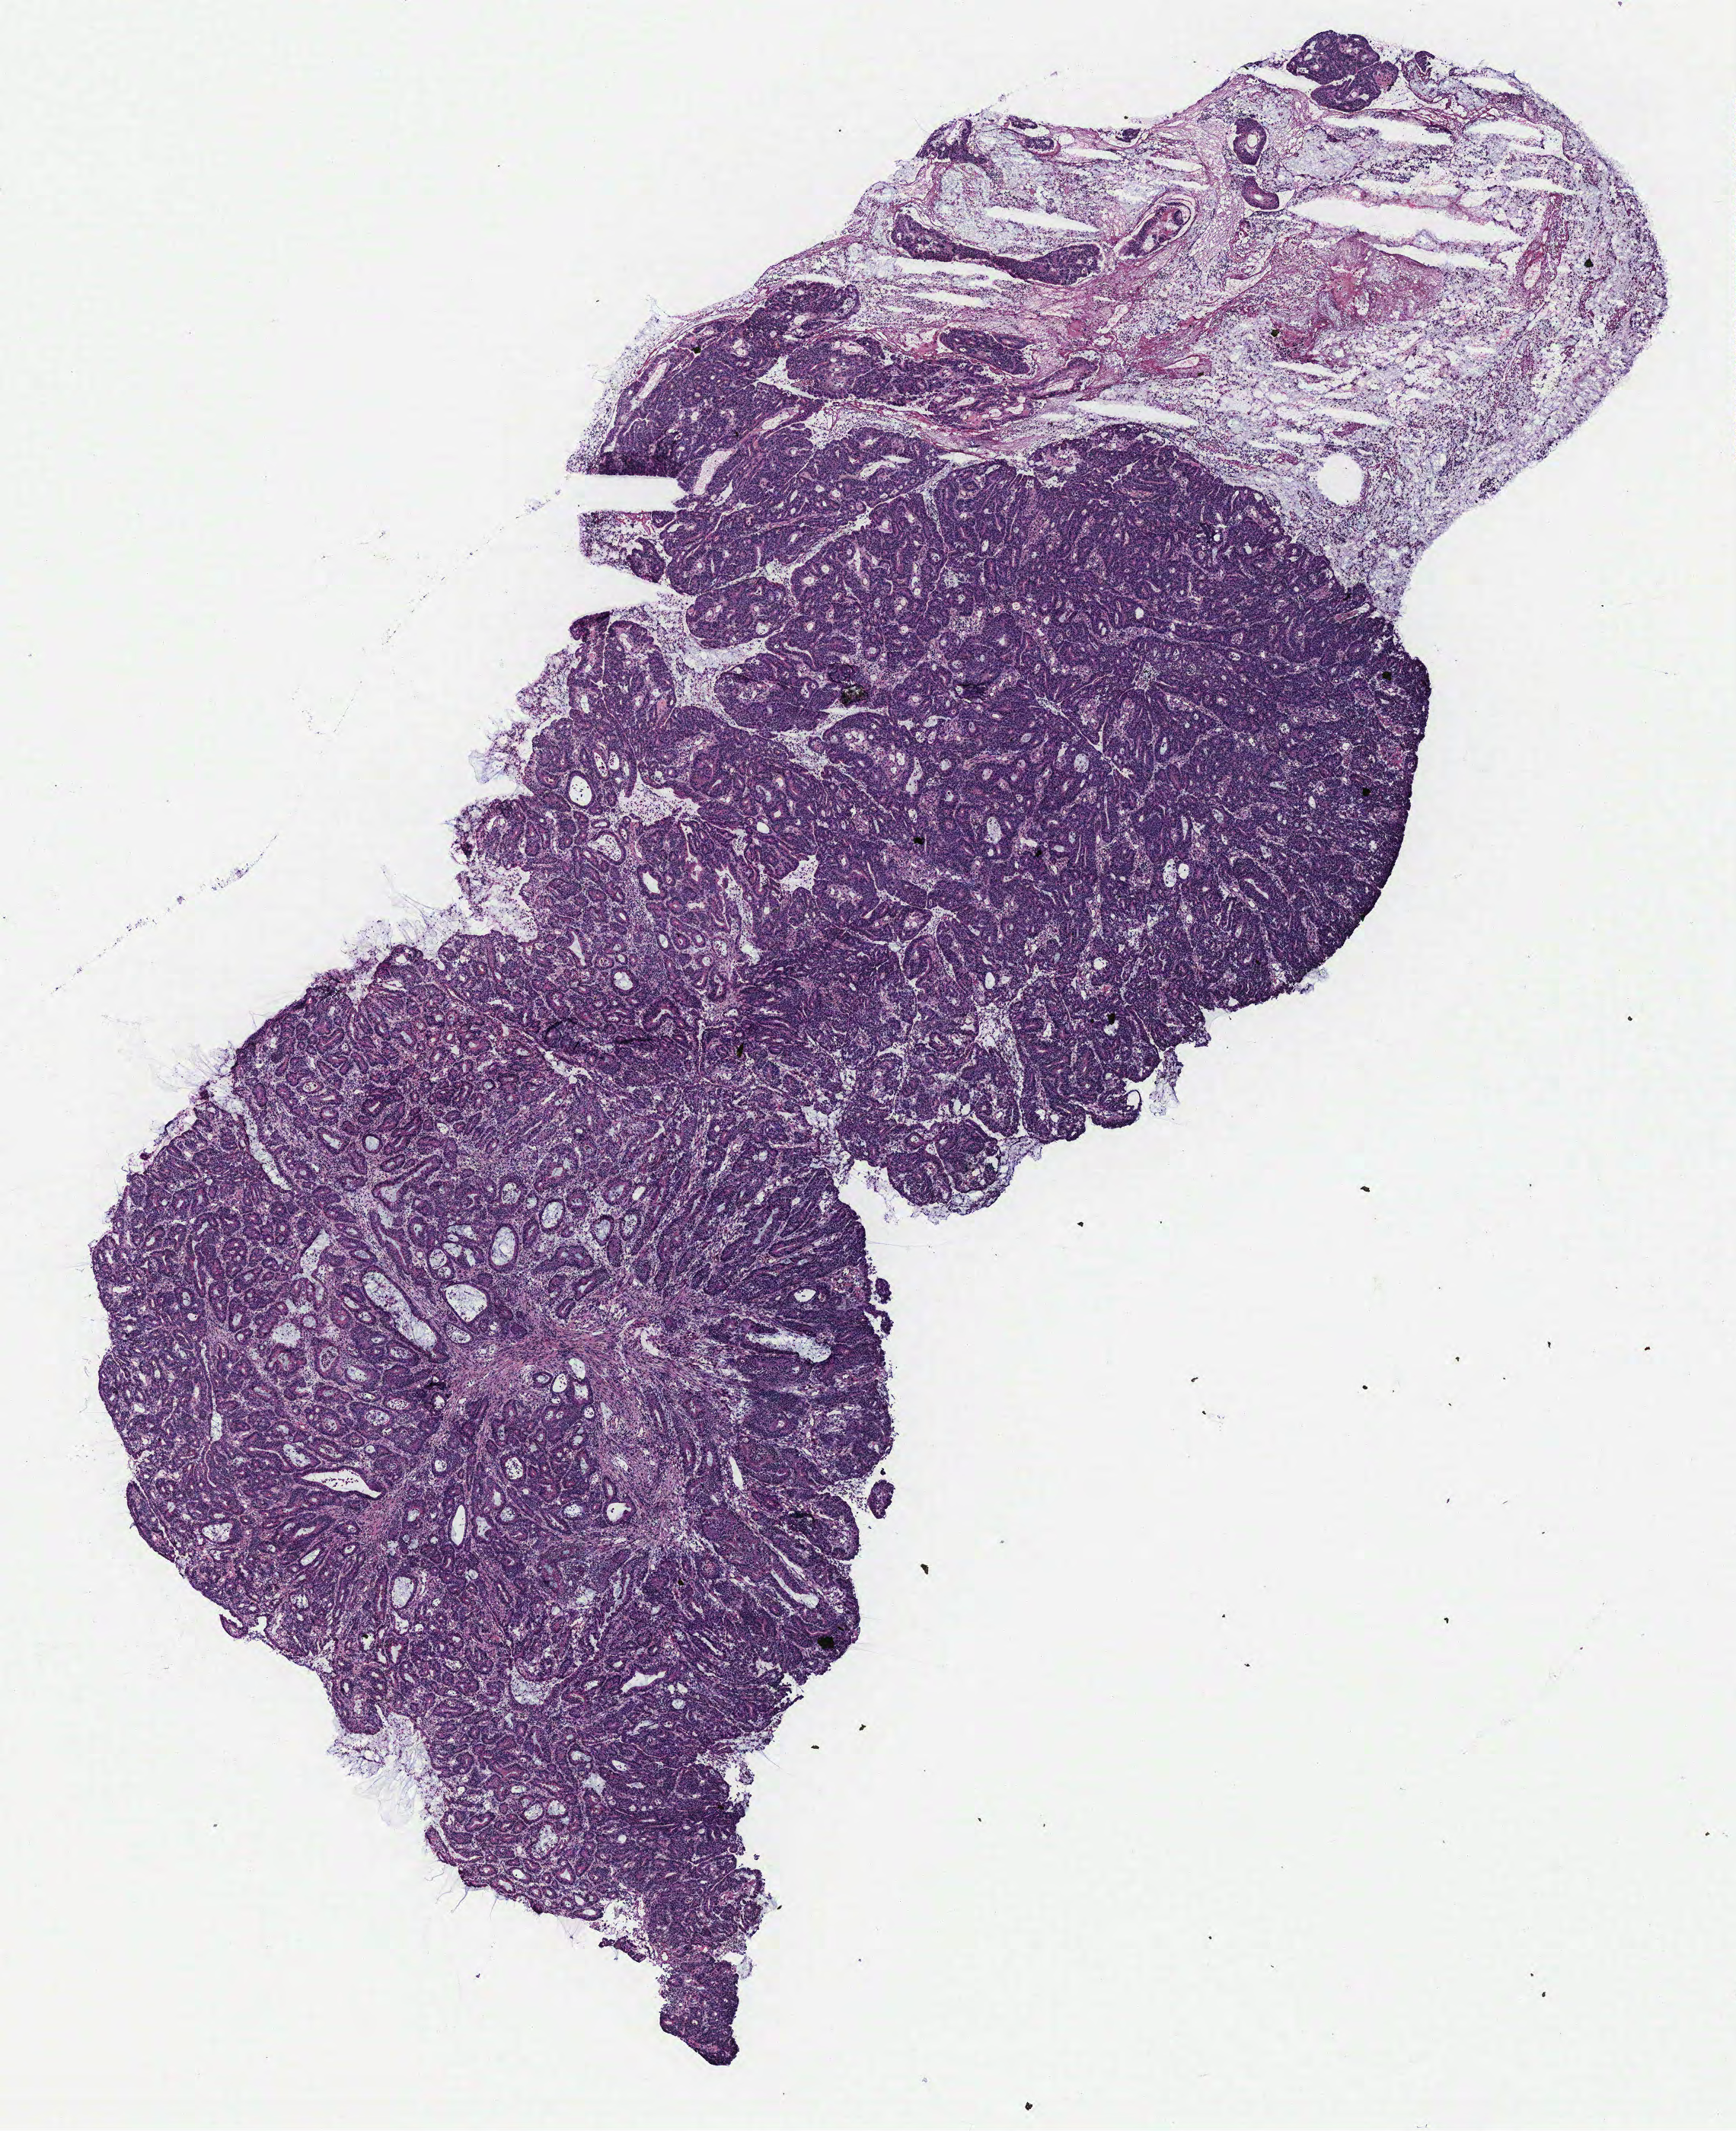
Whole-slide histology image, H&E — shown as a low-resolution overview of the whole scanned area (about 9.1 x 11.2 mm, acquisition: 40x scan), tumour tissue sample, colon. 74-year-old female patient.
Histologic diagnosis: Adenocarcinoma, NOS. AJCC pathologic stage: IIIB. Primary tumour site (as recorded): colon.